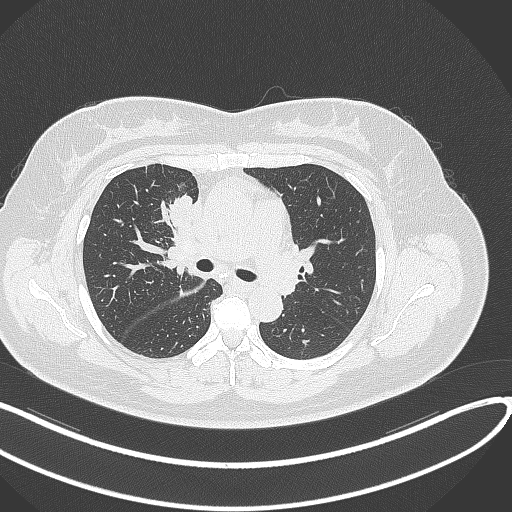
Chest CT, one axial slice. Slice 171 of 303 in the series (ordered by position). 120 kVp. Lung window (W 1500 / L -600 HU). 1 mm slice thickness. 512 × 512 image matrix, field of view 400 × 400 mm. Female patient, age 46 years. Case-level facts recorded for this patient, not image findings: clinical TNM (as recorded): T2a N1 M0.
Annotated regions visible in this slice (rectangle marked by the reading radiologist):
- lung tumour (recorded histology: adenocarcinoma): bounding box (x1, y1, x2, y2) in pixels: (165, 191, 196, 233)